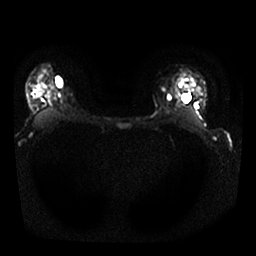
Breast MRI, one axial slice; slice 20 of 25 in the series (ordered by position); diffusion-weighted series; image 2 of 4 stored at this slice position (different b-values; order by instance number); 1.5 T; 256 × 256 image matrix. Female patient.
Annotated regions visible in this slice (expert manual segmentation):
- tumour on diffusion-weighted imaging: bounding box <37,84,46,93> (left, top, right, bottom; pixels)